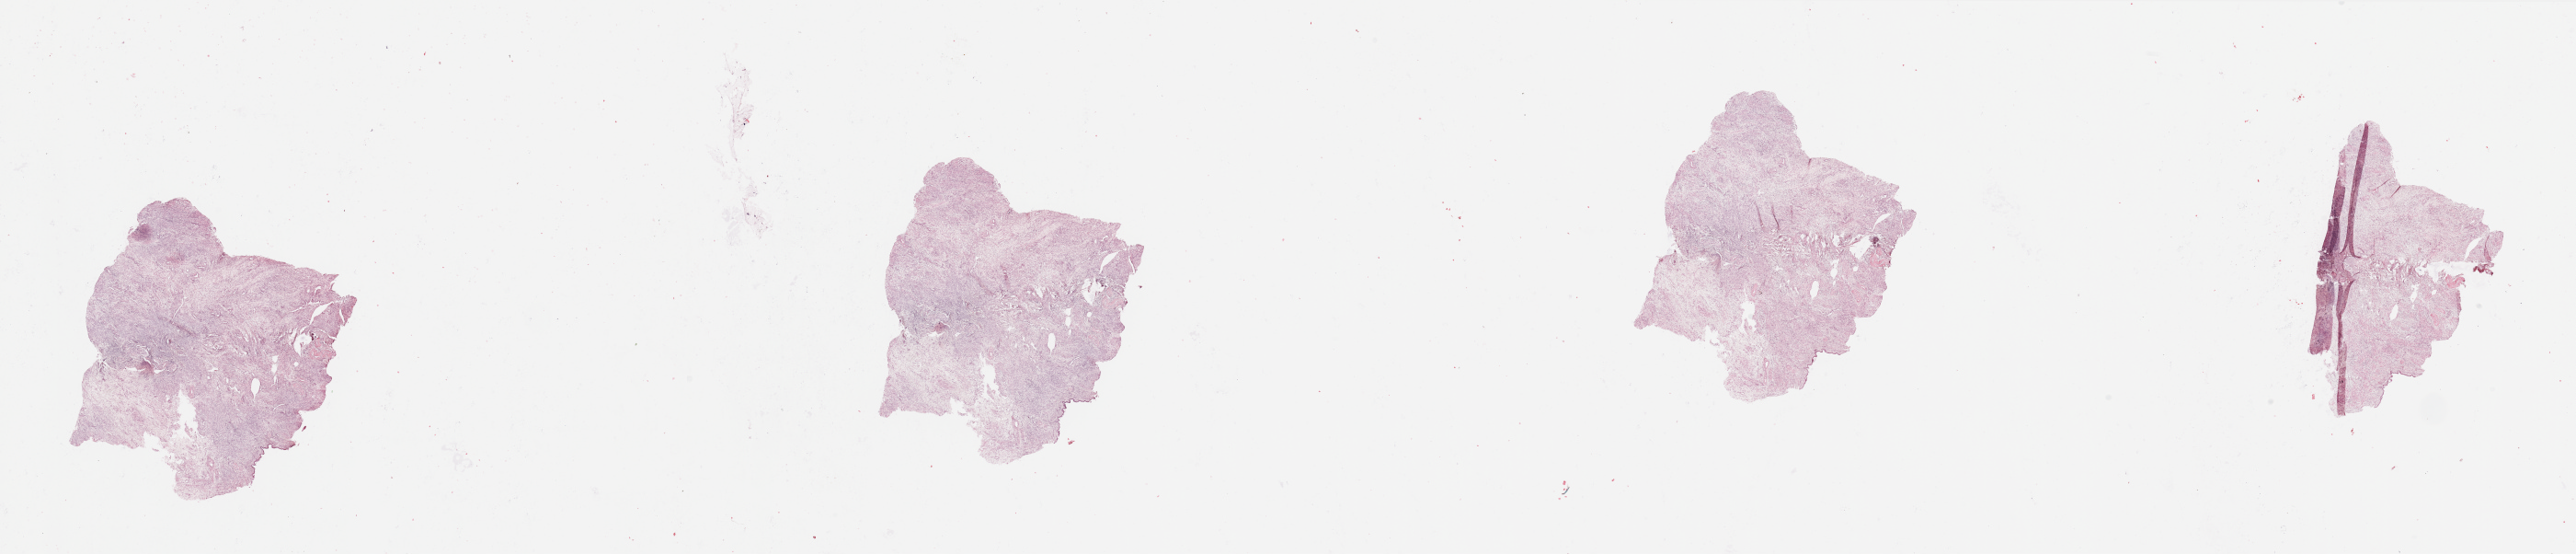
Hematoxylin and eosin (H&E) stained whole-slide image, a low-resolution overview of the entire scanned area, about 44.3 x 9.5 mm, normal (non-tumour) tissue sample, sampled site: uterus. Female, 65 y/o.
This section: normal (non-tumour) tissue from the same patient. Patient diagnosis: Endometrioid adenocarcinoma, NOS.